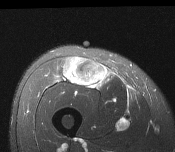
MRI of an extremity soft-tissue mass, one axial slice; position 62 of 116 along the scan axis; T2-weighted fat-saturated; MR volume resampled by the dataset authors to the PET/CT grid (not the native acquisition matrix); 3.27 mm slice thickness; 175 × 152 image matrix, field of view 171 × 148 mm. Male patient. From the clinical record (not read from this slice): histological type: pleiomorphic leiomyosarcoma; grade: intermediate; site of the primary tumour: right thigh.
Structures marked on this image (expert contour drawn on MRI and transferred to this co-registered scan by the dataset authors):
- gross tumour volume including surrounding oedema: box from (x=63, y=58) to (x=109, y=87) px